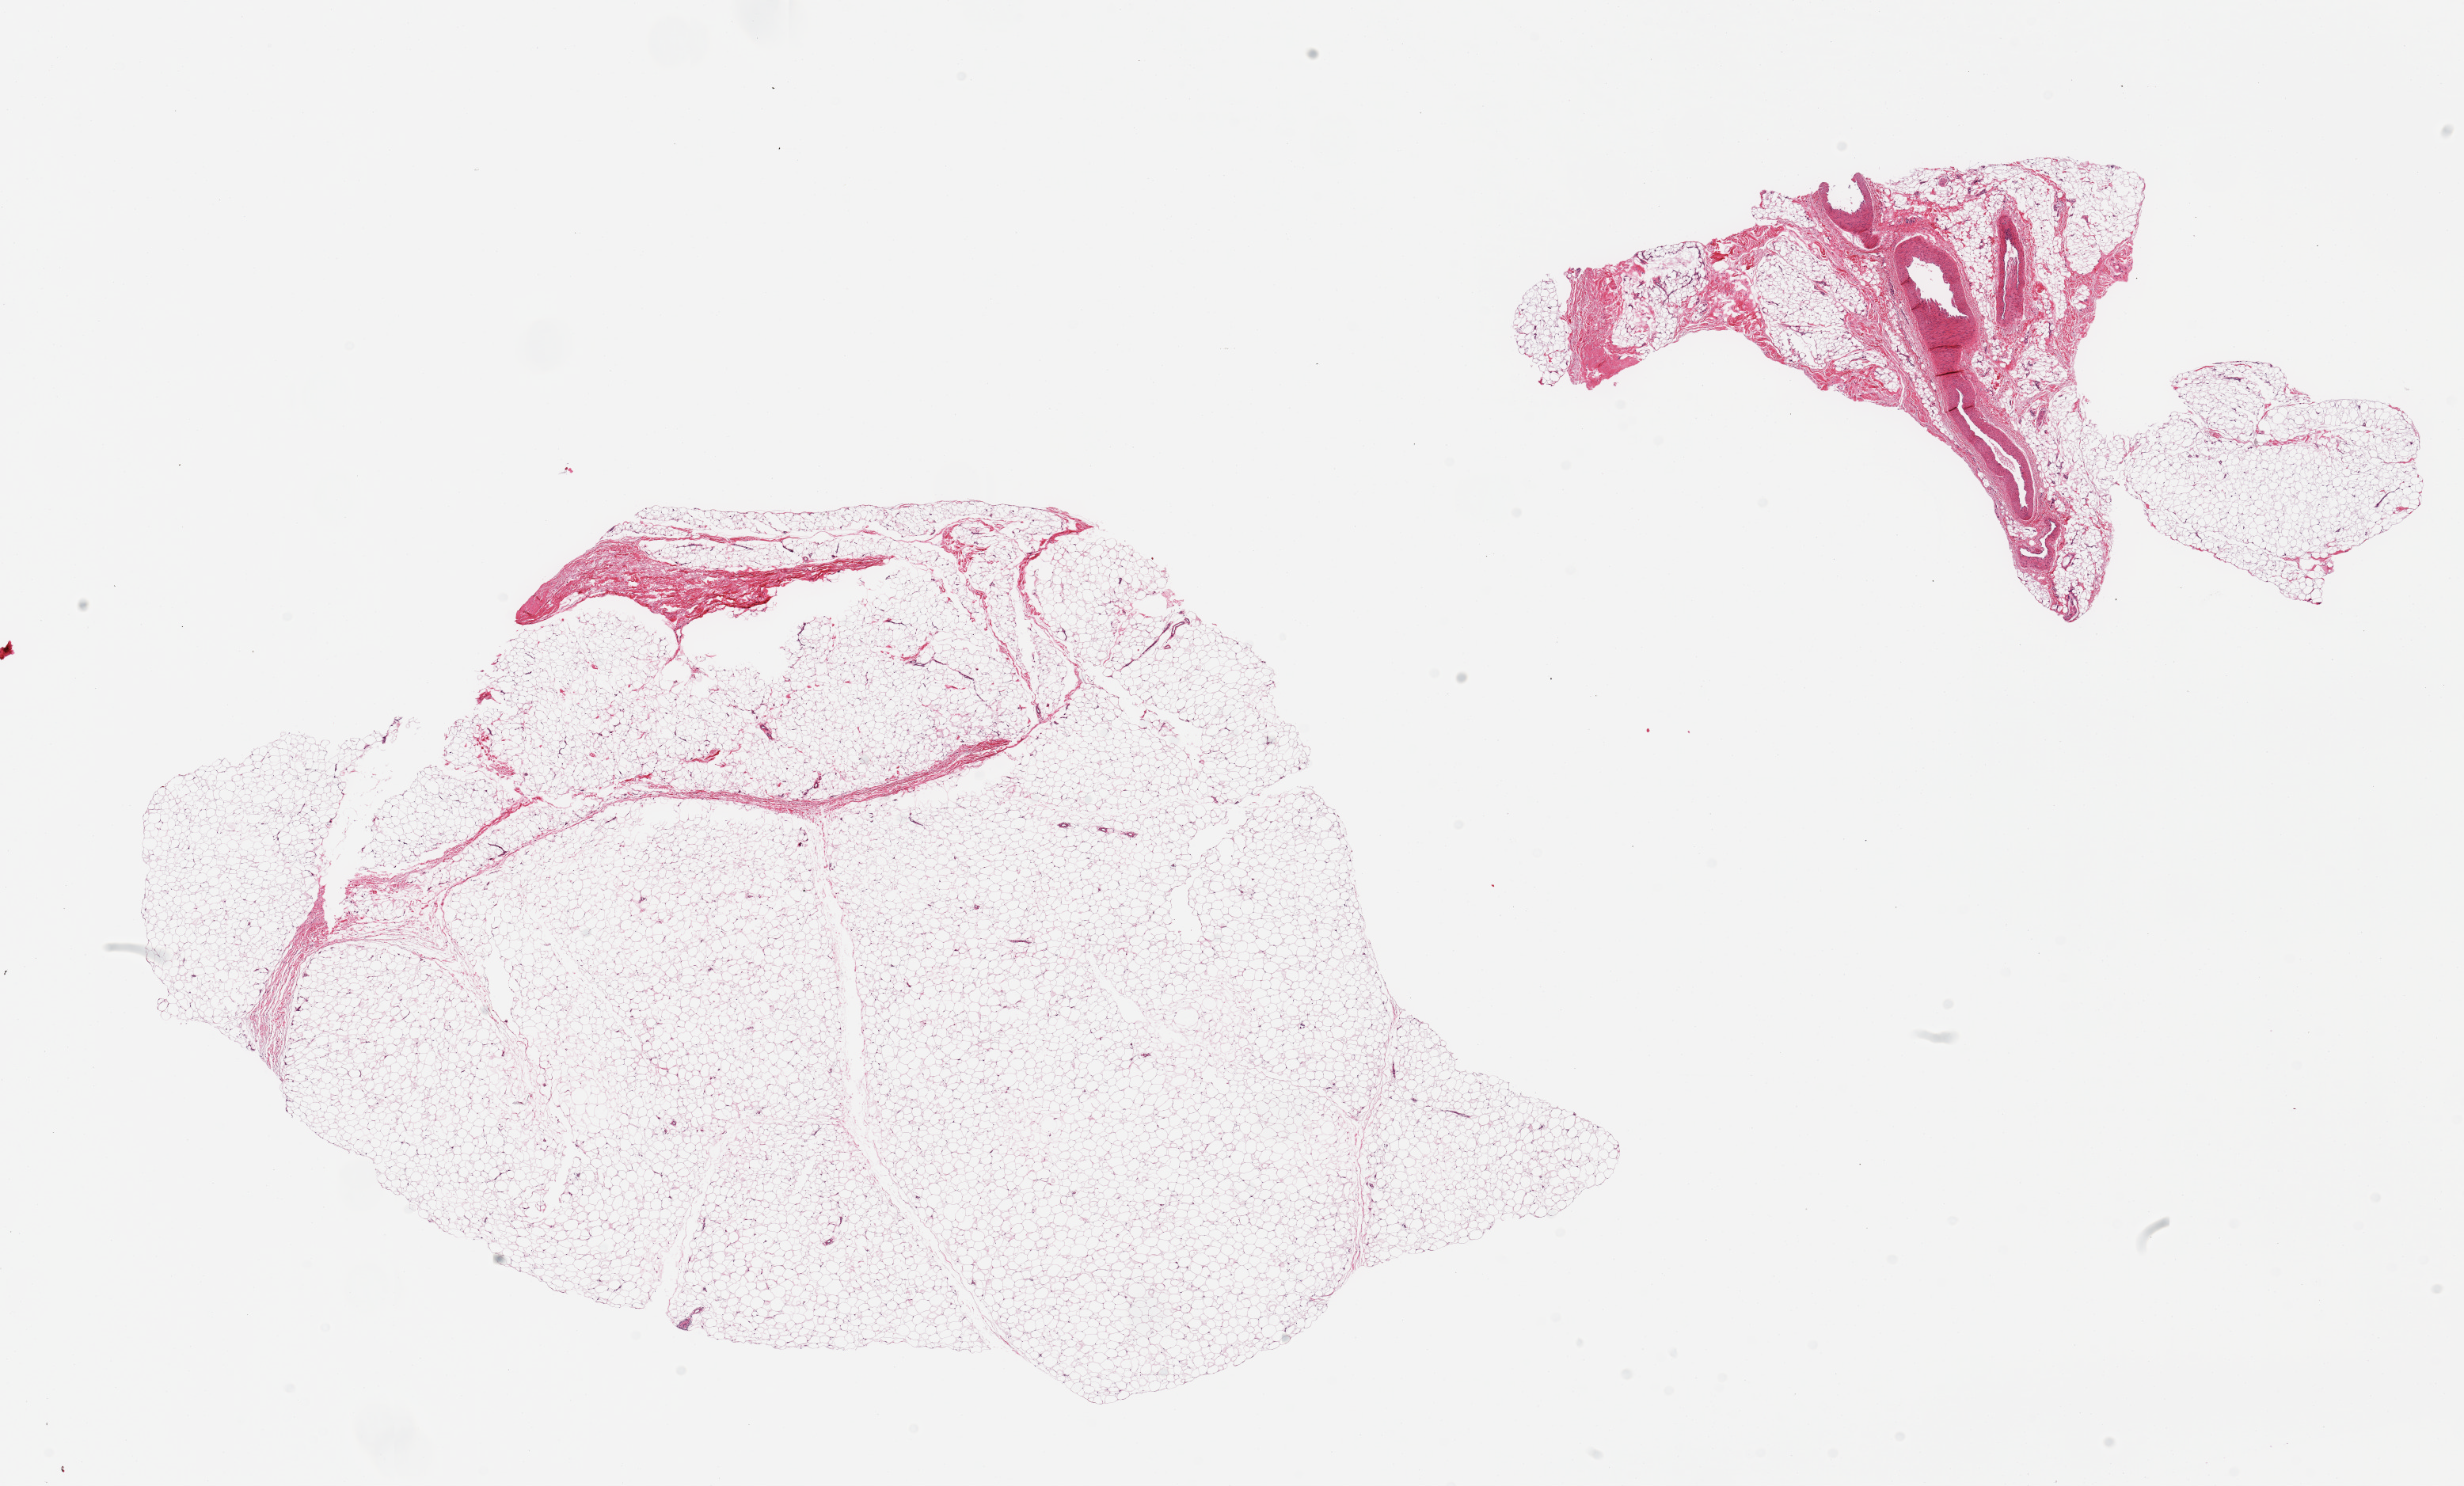
Haematoxylin and eosin whole-slide image, brightfield — a low-resolution overview of the entire scanned area, about 24.6 x 14.8 mm (slide scanned at 20x), PAXgene-fixed, paraffin-embedded tissue, target tissue: adipose tissue, donor tissue sample. Donor sex: male.
Pathologist's review note for this sample: 2 pieces; 1 piece is ~90% fat/10% fibrous, 2nd is ~50% fat/50% fibrous and vessels.